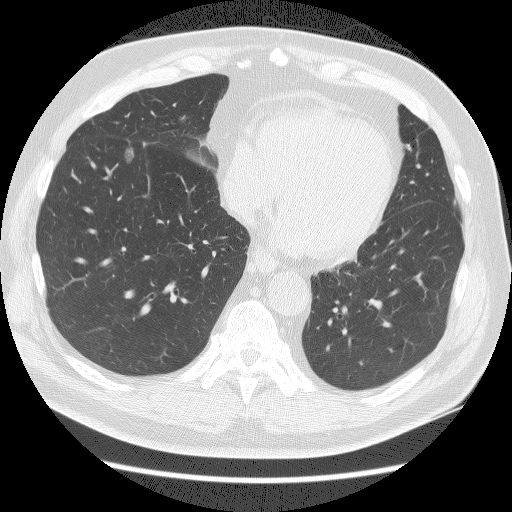
Axial slice from a low-dose chest CT screening exam, baseline annual screen, lung window (W 1500 / L -600 HU), lung (sharp) reconstruction kernel (BONE), 512 × 512 image matrix, field of view 360 × 360 mm. Male participant, aged 65 years at enrolment.
• Expert reader's lesion annotation, bounding box (x1, y1, x2, y2) in pixels: (101, 133, 151, 174).
• The screening reader recorded 3 non-calcified nodules or masses ≥4 mm on this exam (right lower lobe, right middle lobe, left upper lobe); which of them this box marks is not recorded.
• Lung cancer was diagnosed 132 days after this screen: adenocarcinoma, NOS, right lower lobe, poorly differentiated (G3), stage IA (AJCC 6th edition), 10 mm at pathology.